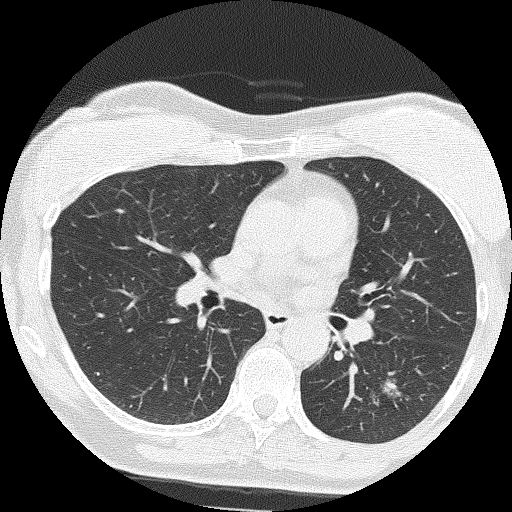
Axial slice from a low-dose chest CT screening exam; second screening round (one year after baseline); lung window (W 1500 / L -600 HU); 2 mm slice thickness; lung (sharp) reconstruction kernel (FC51); slice 72 of 159 in the series; 512 × 512 image matrix, field of view 303 × 303 mm. Female, age 64 years at enrolment. Former smoker at enrolment.
- Lesion marked by an expert reader, bounding box [x1, y1, x2, y2] px = [359, 361, 447, 438].
- The screening reader recorded 3 non-calcified nodules or masses ≥4 mm on this exam; which of them this box marks is not recorded.
- Participant outcome: lung cancer diagnosed 576 days after this screen — adenocarcinoma, NOS, left lower lobe, moderately differentiated (G2), stage IA (AJCC 6th edition), 17 mm at pathology.